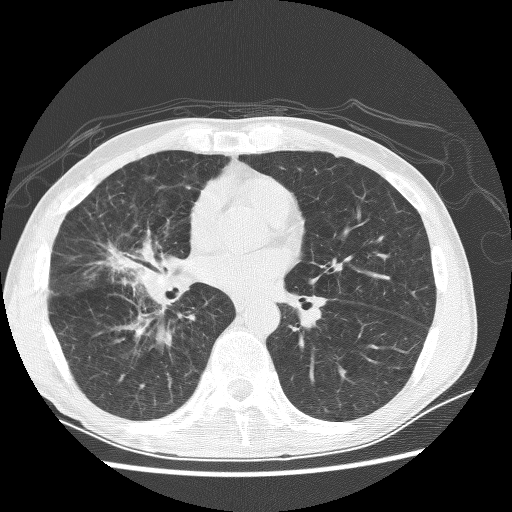
Axial slice from a low-dose chest CT screening exam, baseline screening round, lung window (W 1500 / L -600 HU), 2.5 mm slice thickness, lung (sharp) reconstruction kernel (BONE), 120 kVp, slice 132 of 256 in the series, 512 × 512 image matrix. Male participant, aged 67 years at enrolment. Current smoker at enrolment.
Lesion marked by an expert reader, bounding box [x1, y1, x2, y2] px = [75, 227, 172, 300]. Screening reader's record for this exam (one nodule recorded; not confirmed to be the boxed lesion): non-calcified nodule or mass ≥4 mm, right middle lobe, 28 × 18 mm, spiculated (stellate) margins, soft tissue attenuation. Official screen result: positive, change unspecified: nodule(s) >= 4 mm or enlarging nodule(s), mass(es), or other non-specific abnormalities suspicious for lung cancer. Participant outcome: lung cancer diagnosed 69 days after this screen — adenocarcinoma, NOS, right middle lobe, stage IV (AJCC 6th edition), 60 mm at pathology.